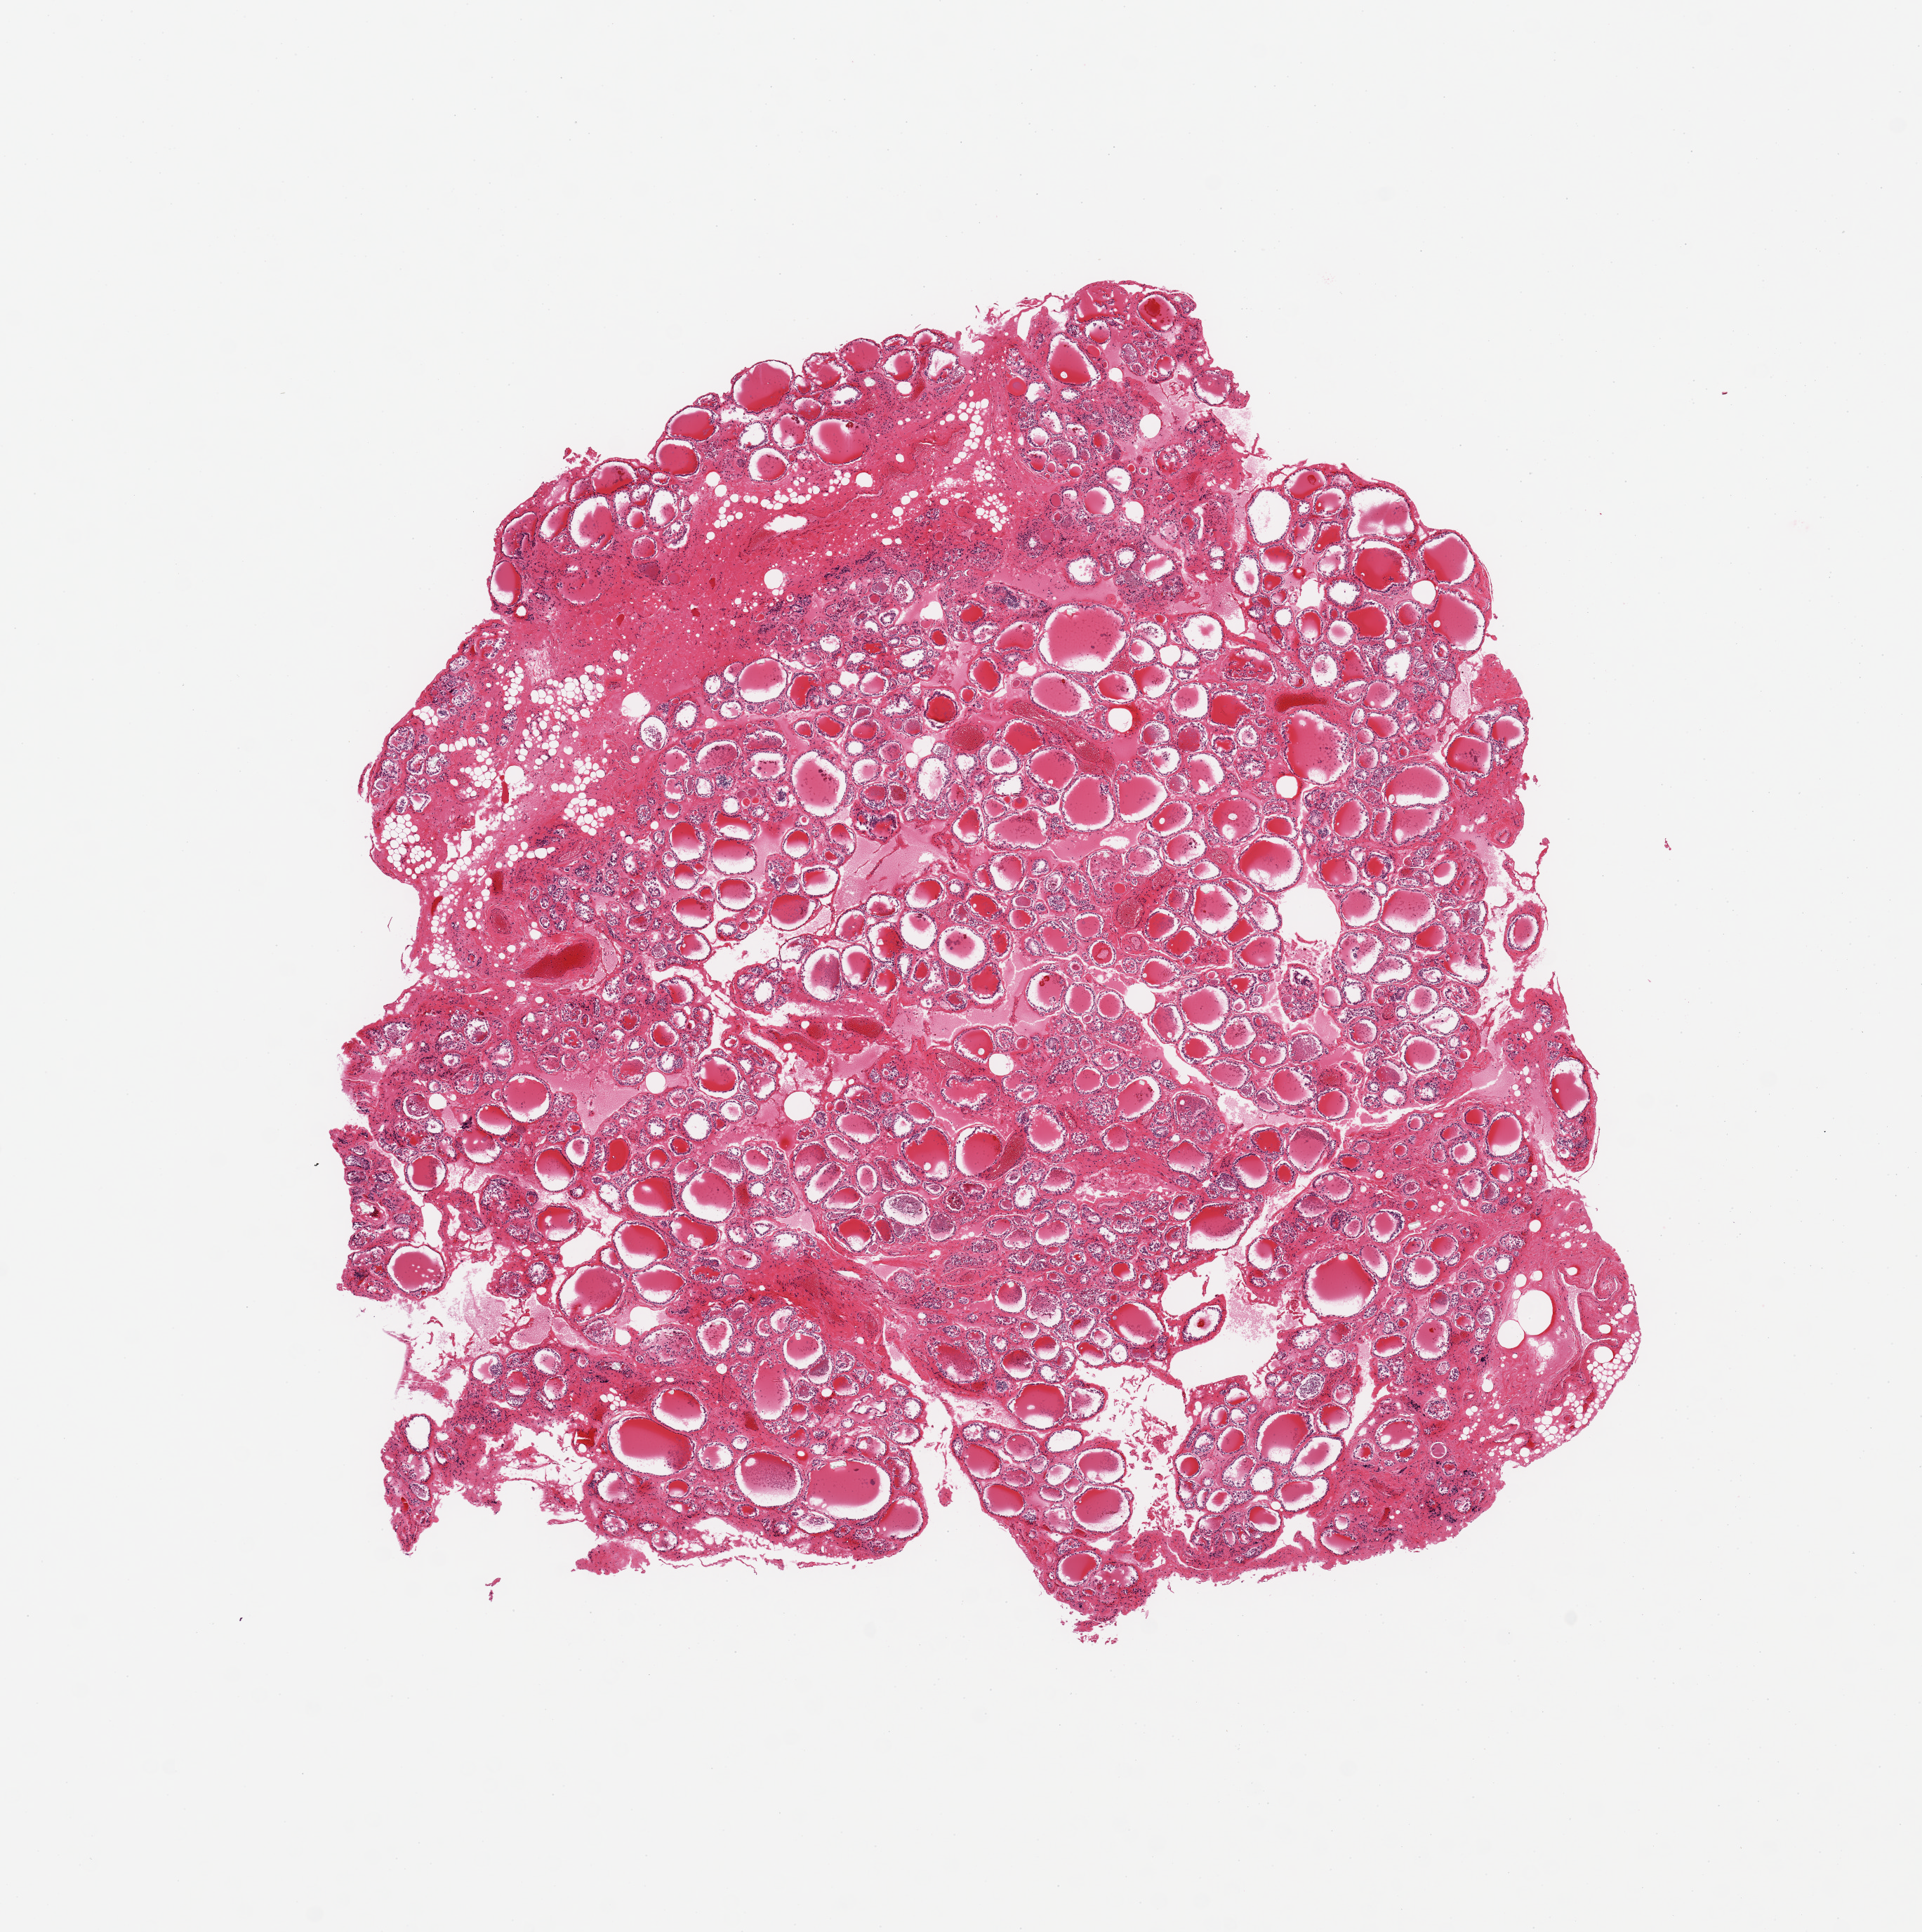
Whole-slide image, hematoxylin and eosin (H&E) stain, brightfield — a low-resolution overview of the entire scanned area, about 10.8 x 10.9 mm; PAXgene-fixed paraffin-embedded (PFPE) section; sampled site (target tissue): thyroid; tissue donor sample. Male donor.
Reviewer comment on this tissue sample: 1 piece; 10% fibrous content.